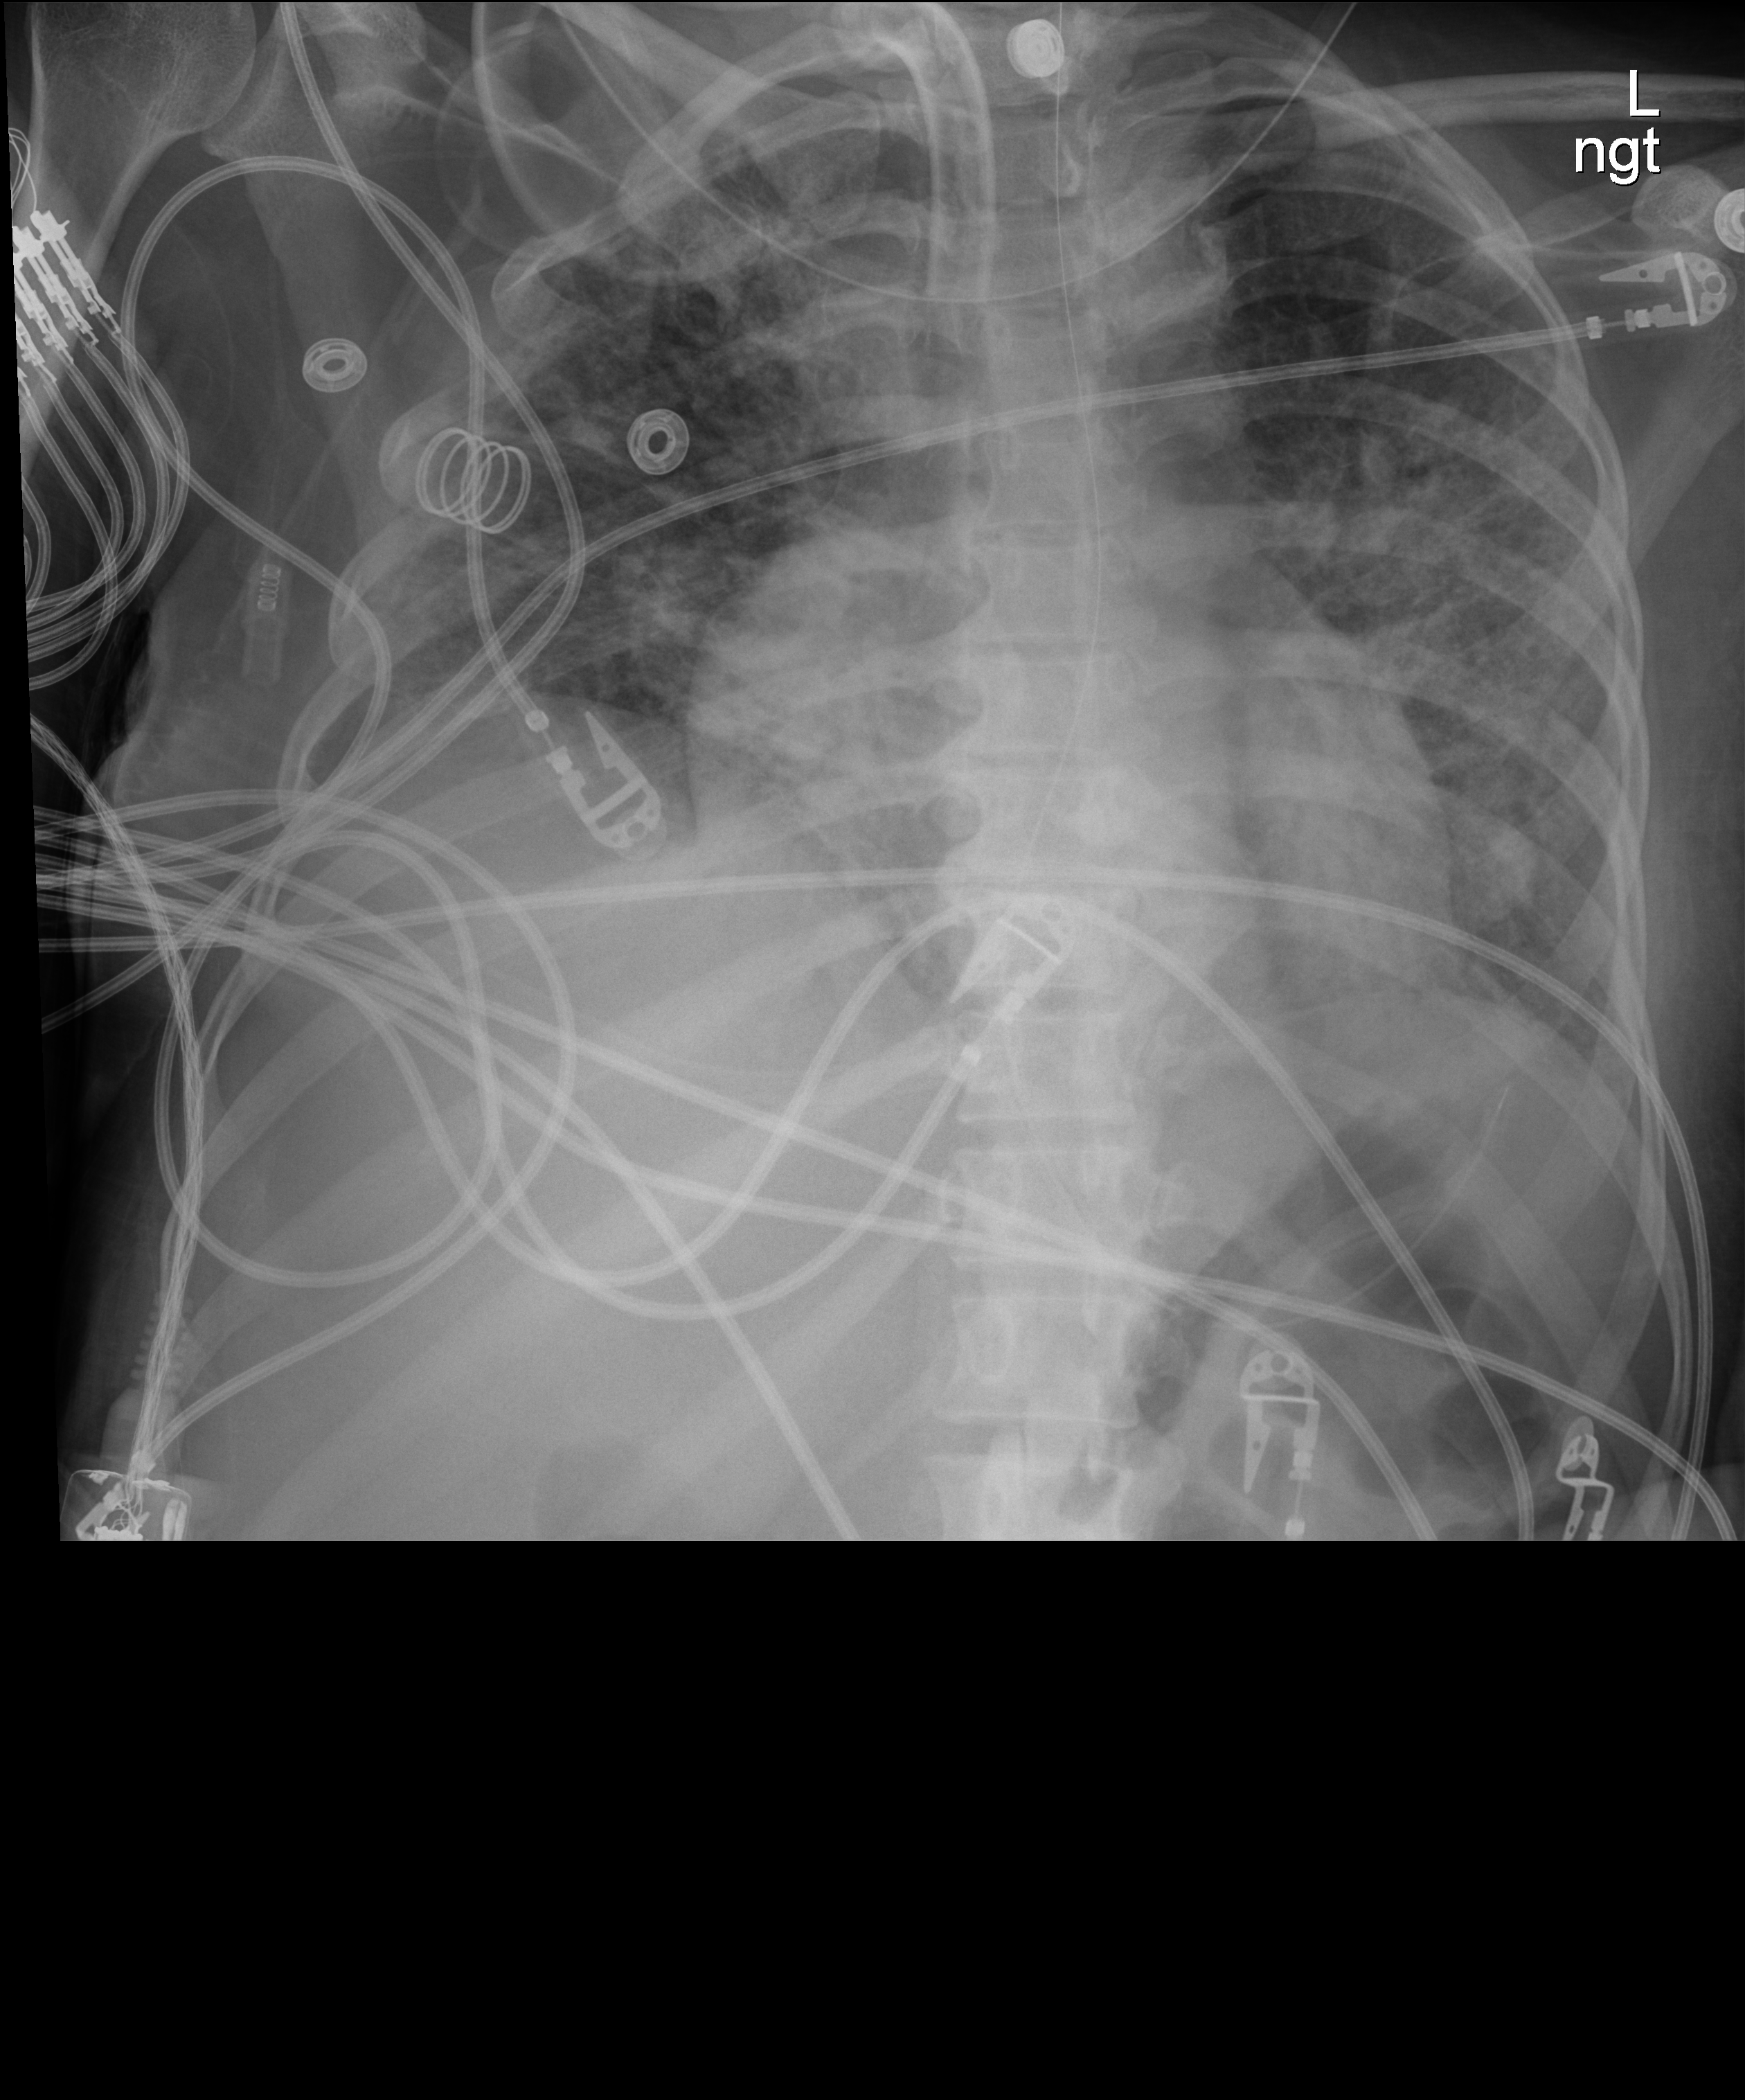
Chest radiograph (digital radiography); anteroposterior (AP) projection. Female patient hospitalised with COVID-19, age 18–59 years.
Hospital-stay facts (about this admission, not read from this image; timing relative to this image not recorded): diabetes (admission record): no; admitted to intensive care during this hospital stay: yes; mechanically ventilated during this hospital stay: yes.